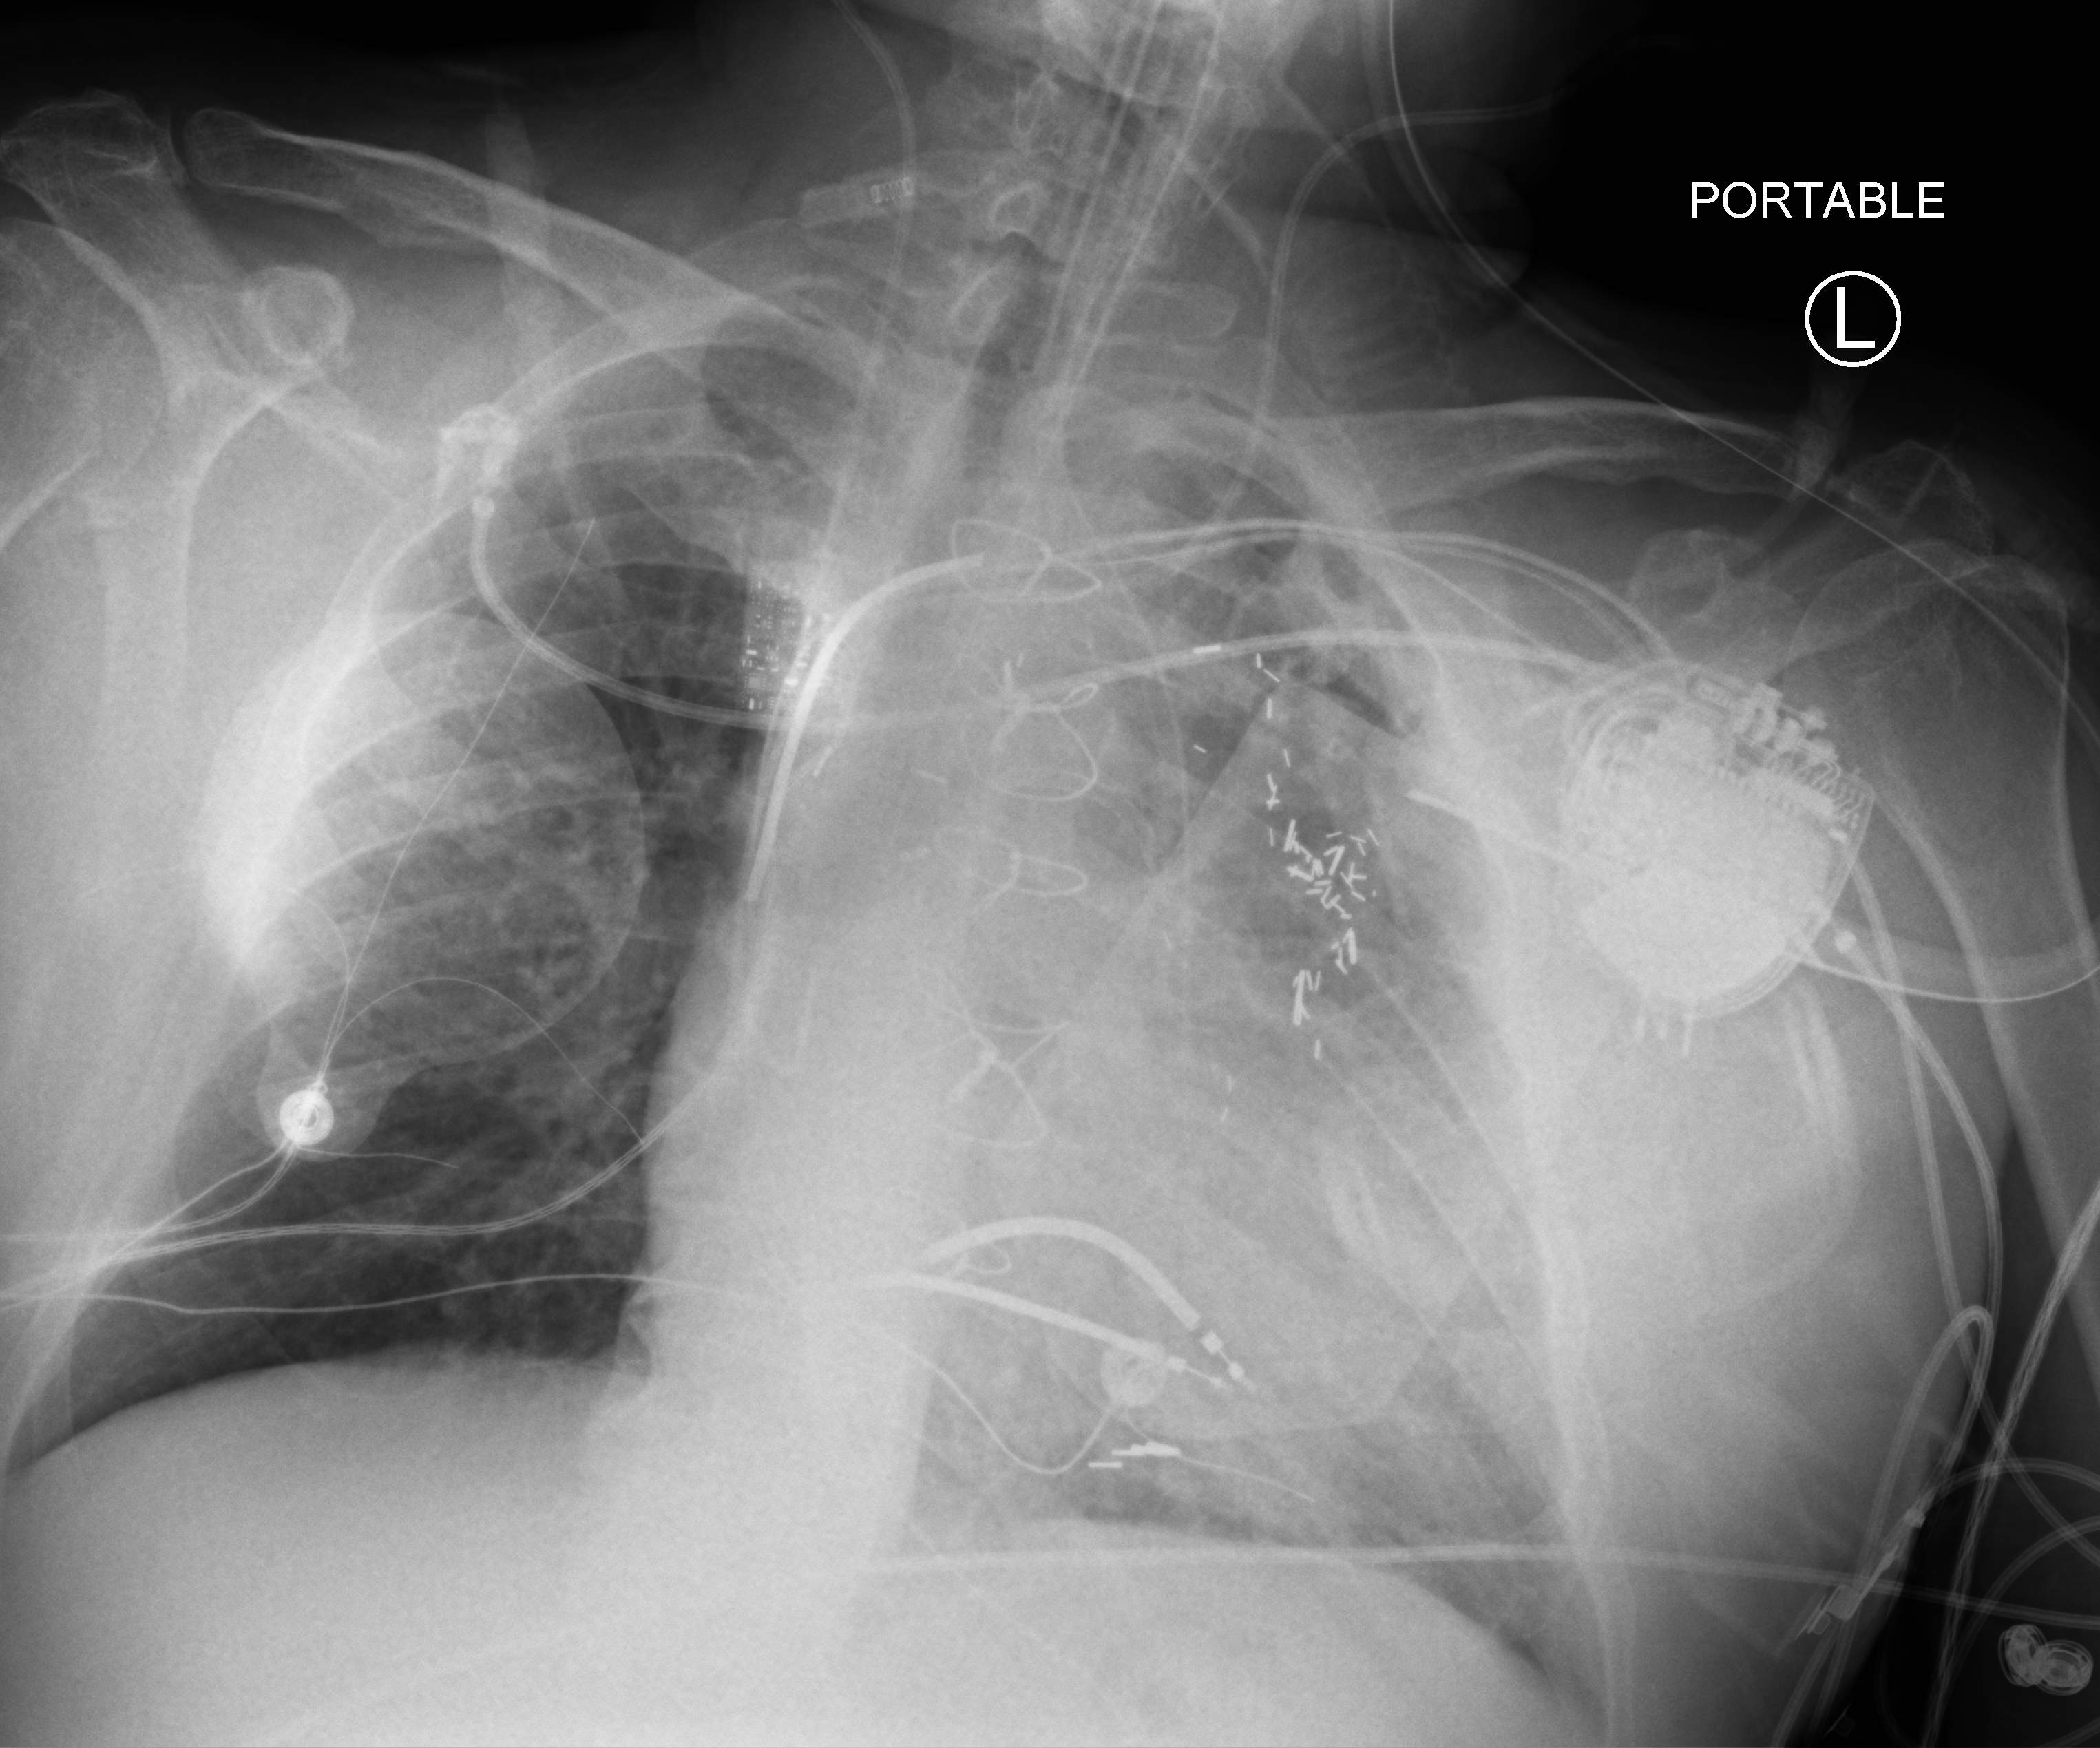
Portable chest radiograph; anteroposterior (AP) projection. Male patient hospitalised with COVID-19, age 60–74 years.
Hospital-stay facts (about this admission, not read from this image; timing relative to this image not recorded): admitted to intensive care during this hospital stay: yes; mechanically ventilated during this hospital stay: yes.